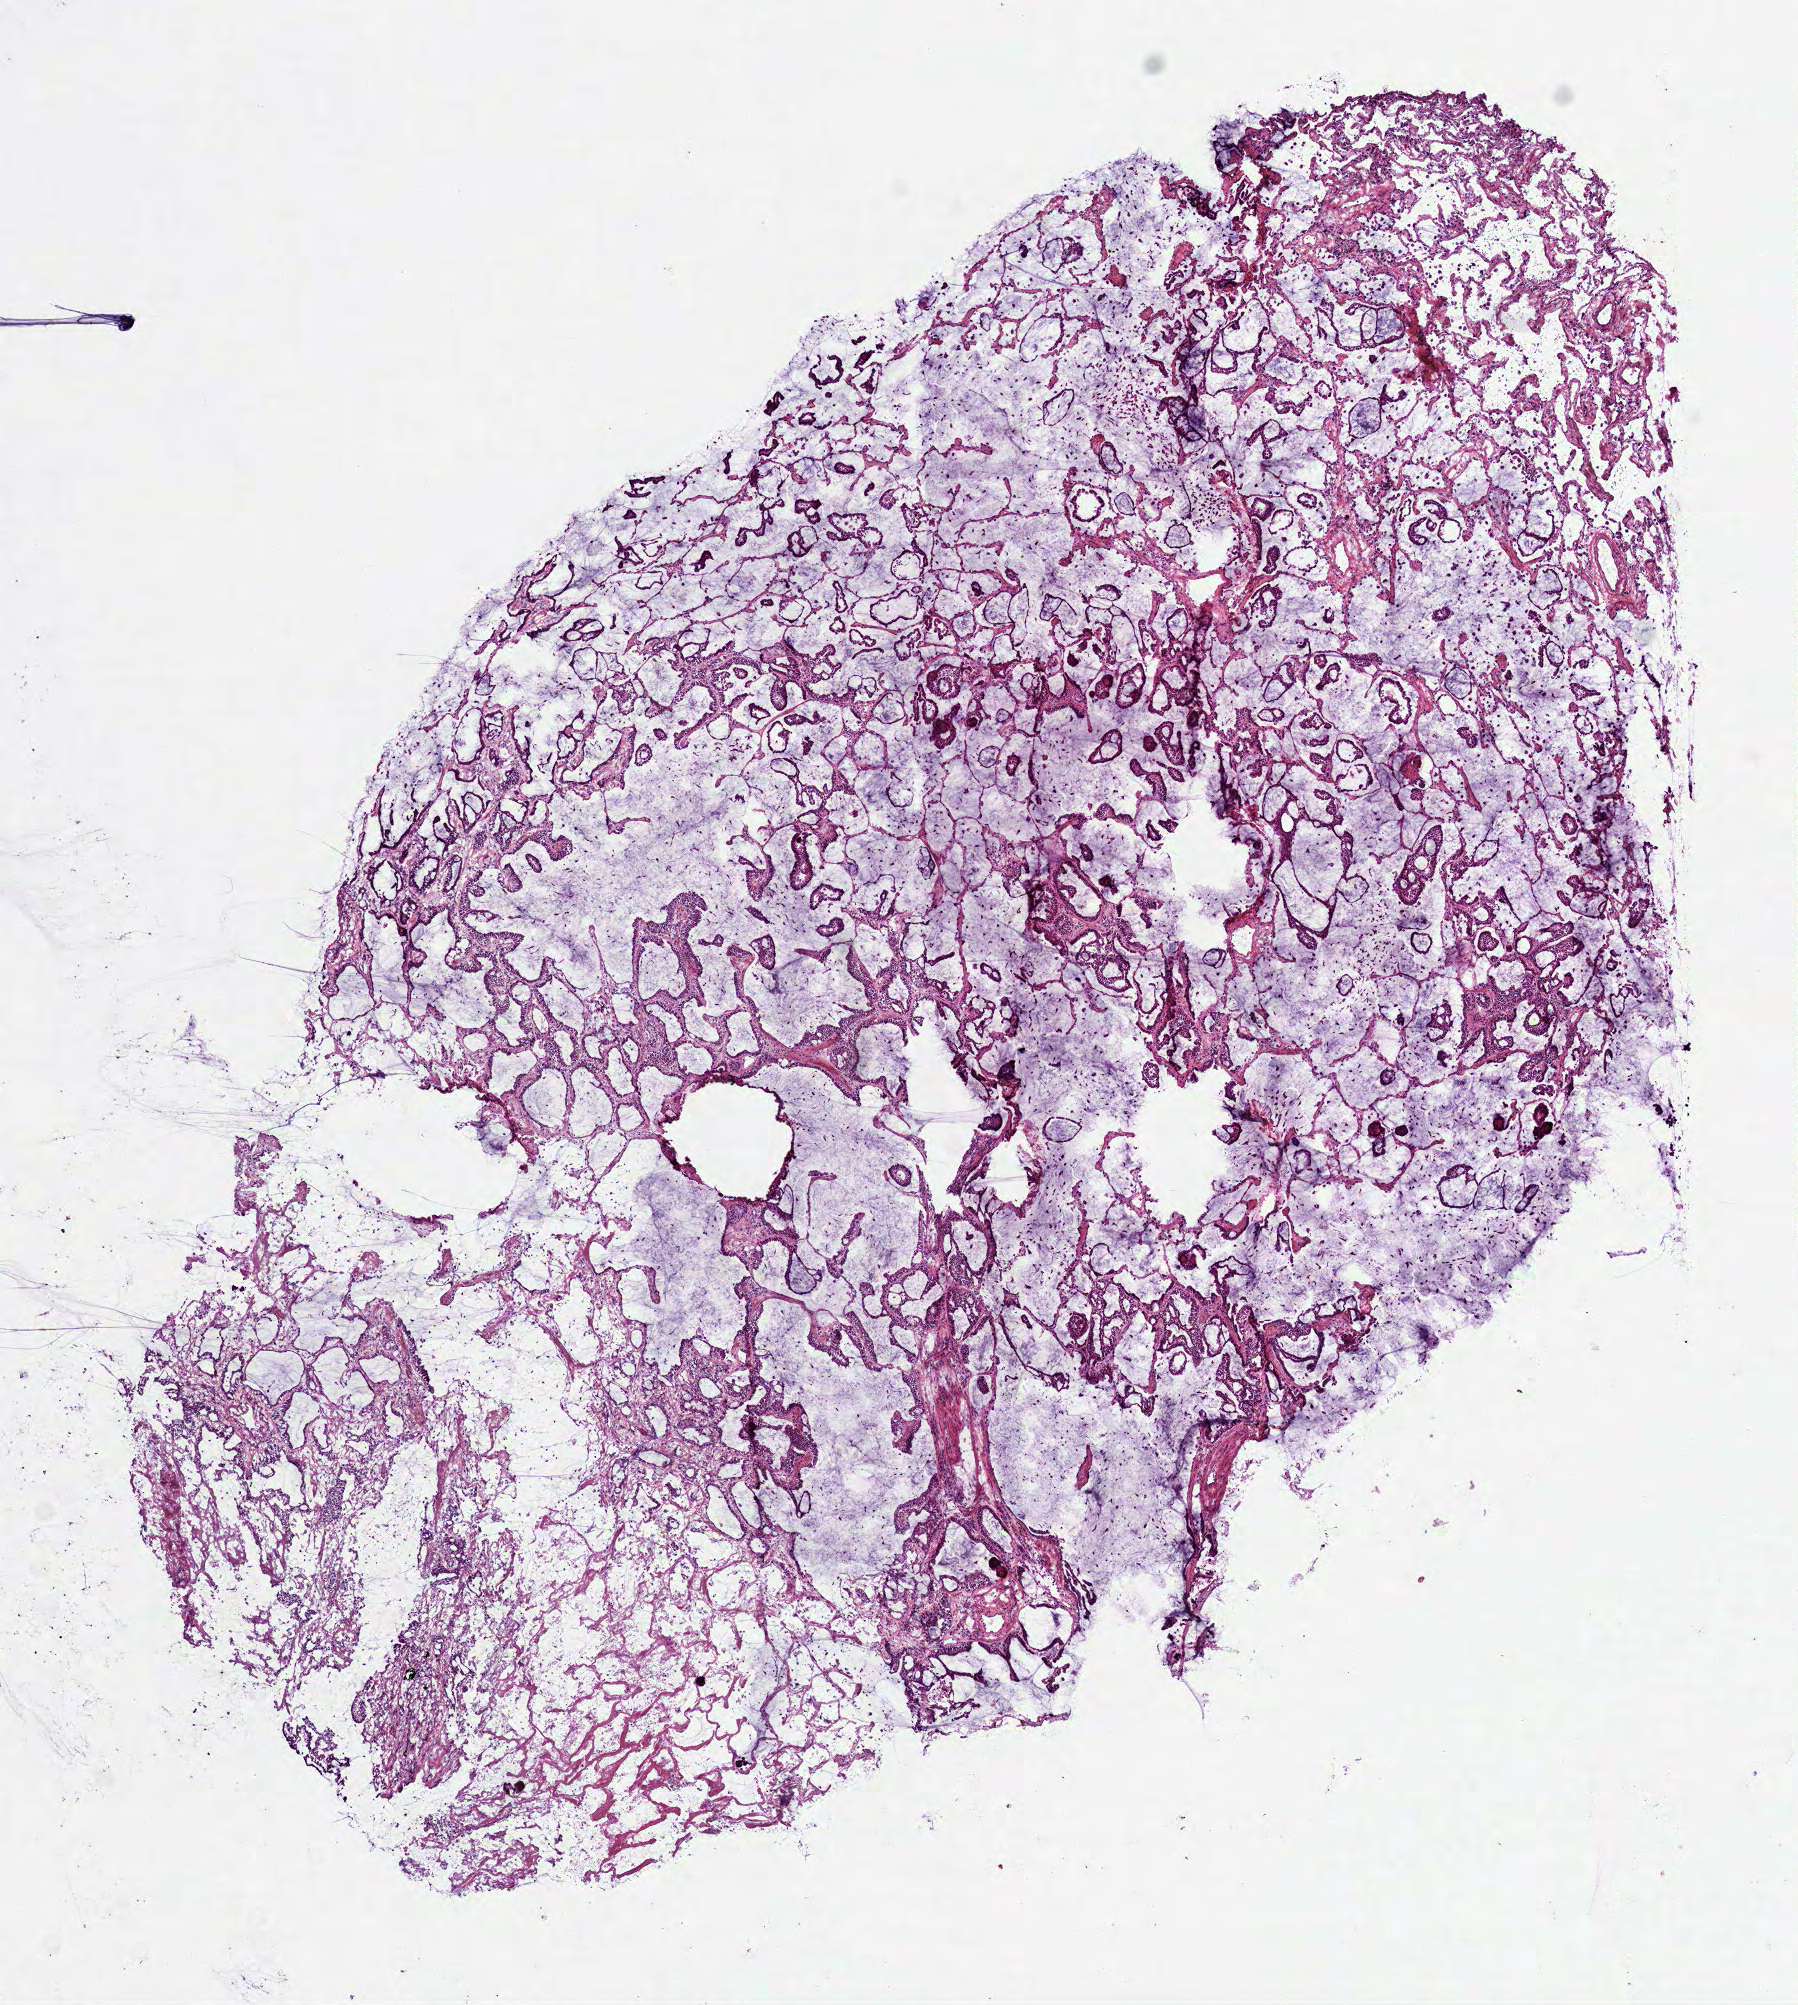
Whole-slide histology image, H&E-stained — a low-resolution overview of the entire scanned area, about 7.3 x 8.1 mm (acquisition: 40x scan), frozen section from the top of the tissue portion, lung, primary tumour sample. Female, age 60 years at initial diagnosis. Slide review estimates, as recorded: tumour cells 85%, tumour nuclei 80%, normal cells 0%, stromal cells 15%, necrosis 0%.
AJCC pathologic stage: IA. Laterality: right. Diagnosis: Bronchio-alveolar carcinoma, mucinous (upper lobe, lung).